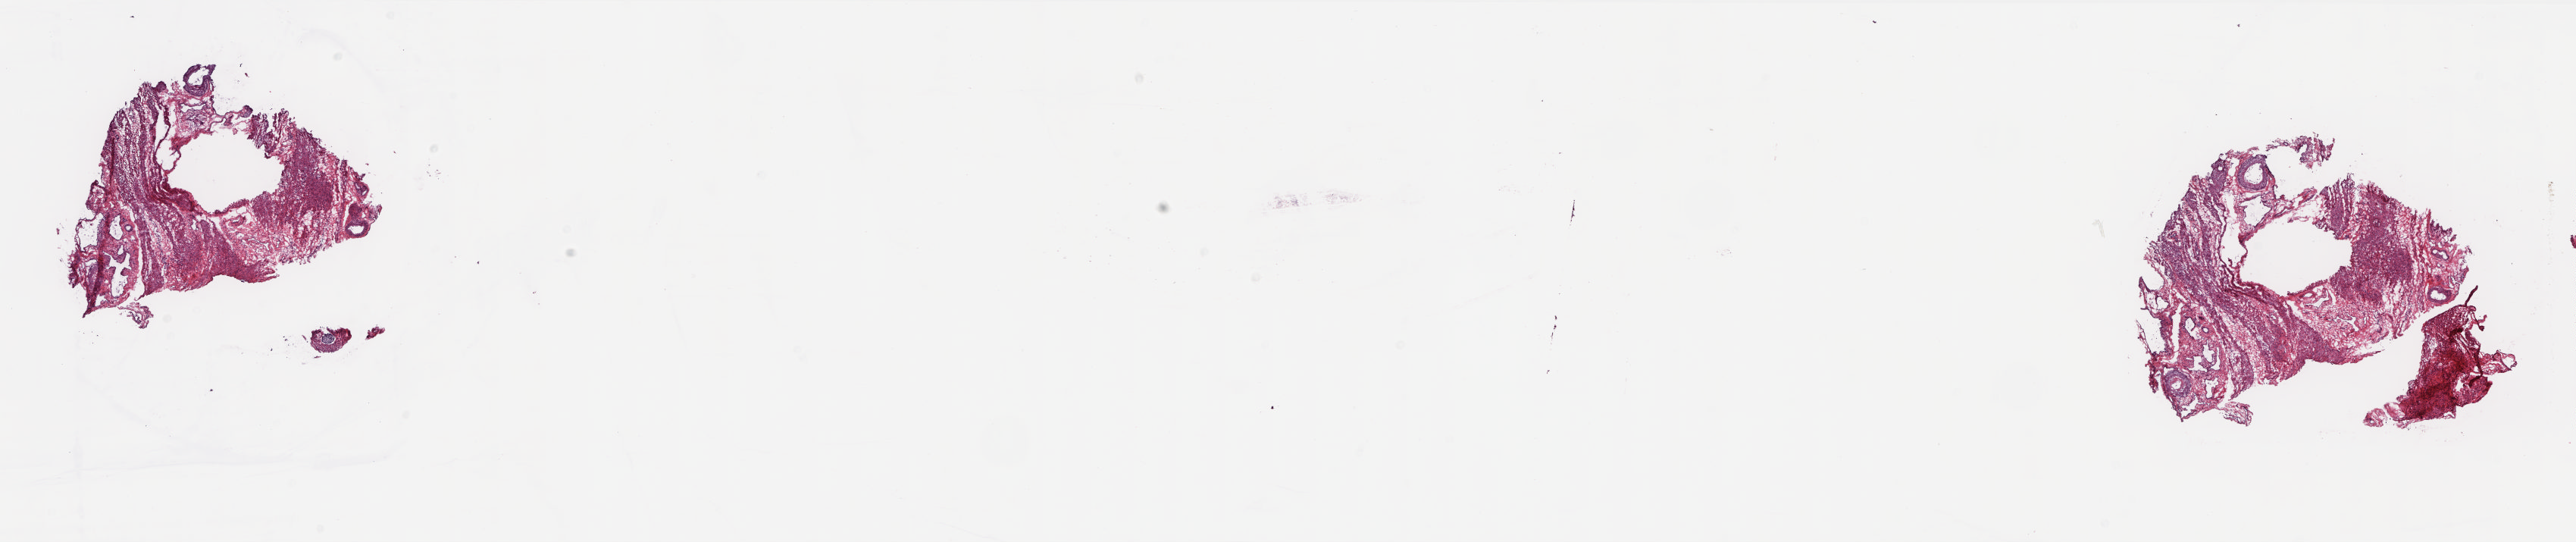
Whole-slide histology image, H&E-stained — a low-resolution overview of the entire scanned area, about 27.4 x 5.8 mm; frozen section from the top of the tissue portion; solid tissue normal (non-tumour tissue) sample from the cervix. Patient: female, age at initial diagnosis 68 years. Slide review estimates, as recorded: tumour cells 0%, tumour nuclei 0%, normal cells 100%, stromal cells 0%, necrosis 0%. Inflammatory infiltration, as recorded: lymphocyte infiltration 1%, monocyte infiltration 0%, neutrophil infiltration 0%.
This section: solid tissue normal sample (biorepository sample class). Patient diagnosis: Squamous cell carcinoma, keratinizing, NOS.